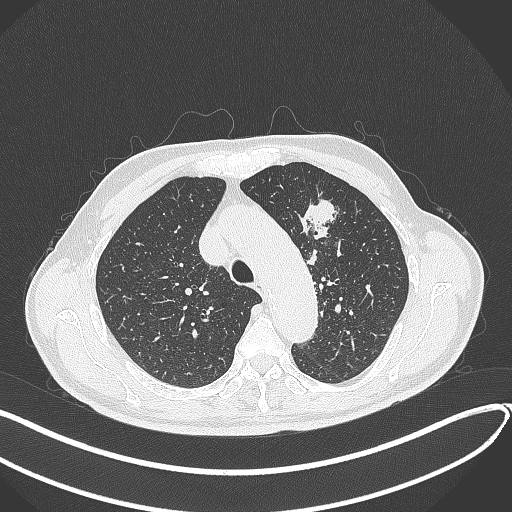
Chest CT, one axial slice; position 312 of 459 along the scan axis; reconstruction kernel B70f; 120 kVp; lung window (W 1500 / L -600 HU); 1 mm slice thickness; 512 × 512 image matrix, field of view 400 × 400 mm. Male patient, age 74 years. Case-level facts recorded for this patient, not image findings: clinical TNM (as recorded): T2b N0 M1c.
Structures marked on this image (bounding box drawn by a radiologist):
- lung tumour (recorded histology: adenocarcinoma): bounding box <298,195,341,247> (left, top, right, bottom; pixels)